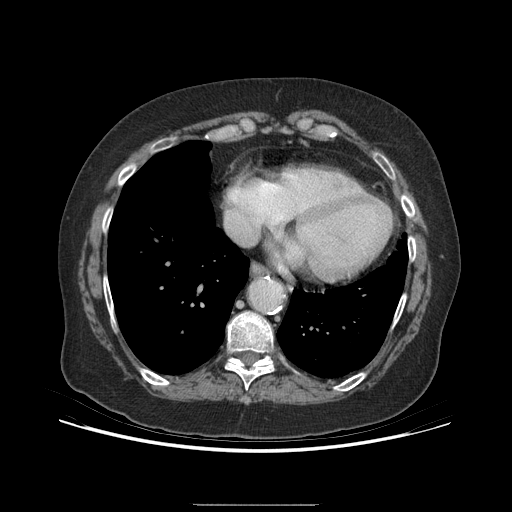
Contrast-enhanced abdominal CT (liver protocol), one axial slice; slice 188 of 192 in the series (ordered by position); 140 kVp; soft-tissue window (W 400 / L 40 HU); 512 × 512 image matrix, field of view 400 × 400 mm. Case-level facts recorded for this patient, not image findings: diagnosis: hepatocellular carcinoma (patient treated with transarterial chemoembolisation; whether this scan precedes or follows treatment is not stated here); TNM stage (as recorded): Stage-I; Child-Pugh class: A; tumour nodularity: uninodular.
Structures marked on this image (semi-automatic segmentation, software-assisted and operator-edited):
- abdominal aorta: box from (x=251, y=280) to (x=280, y=310) px